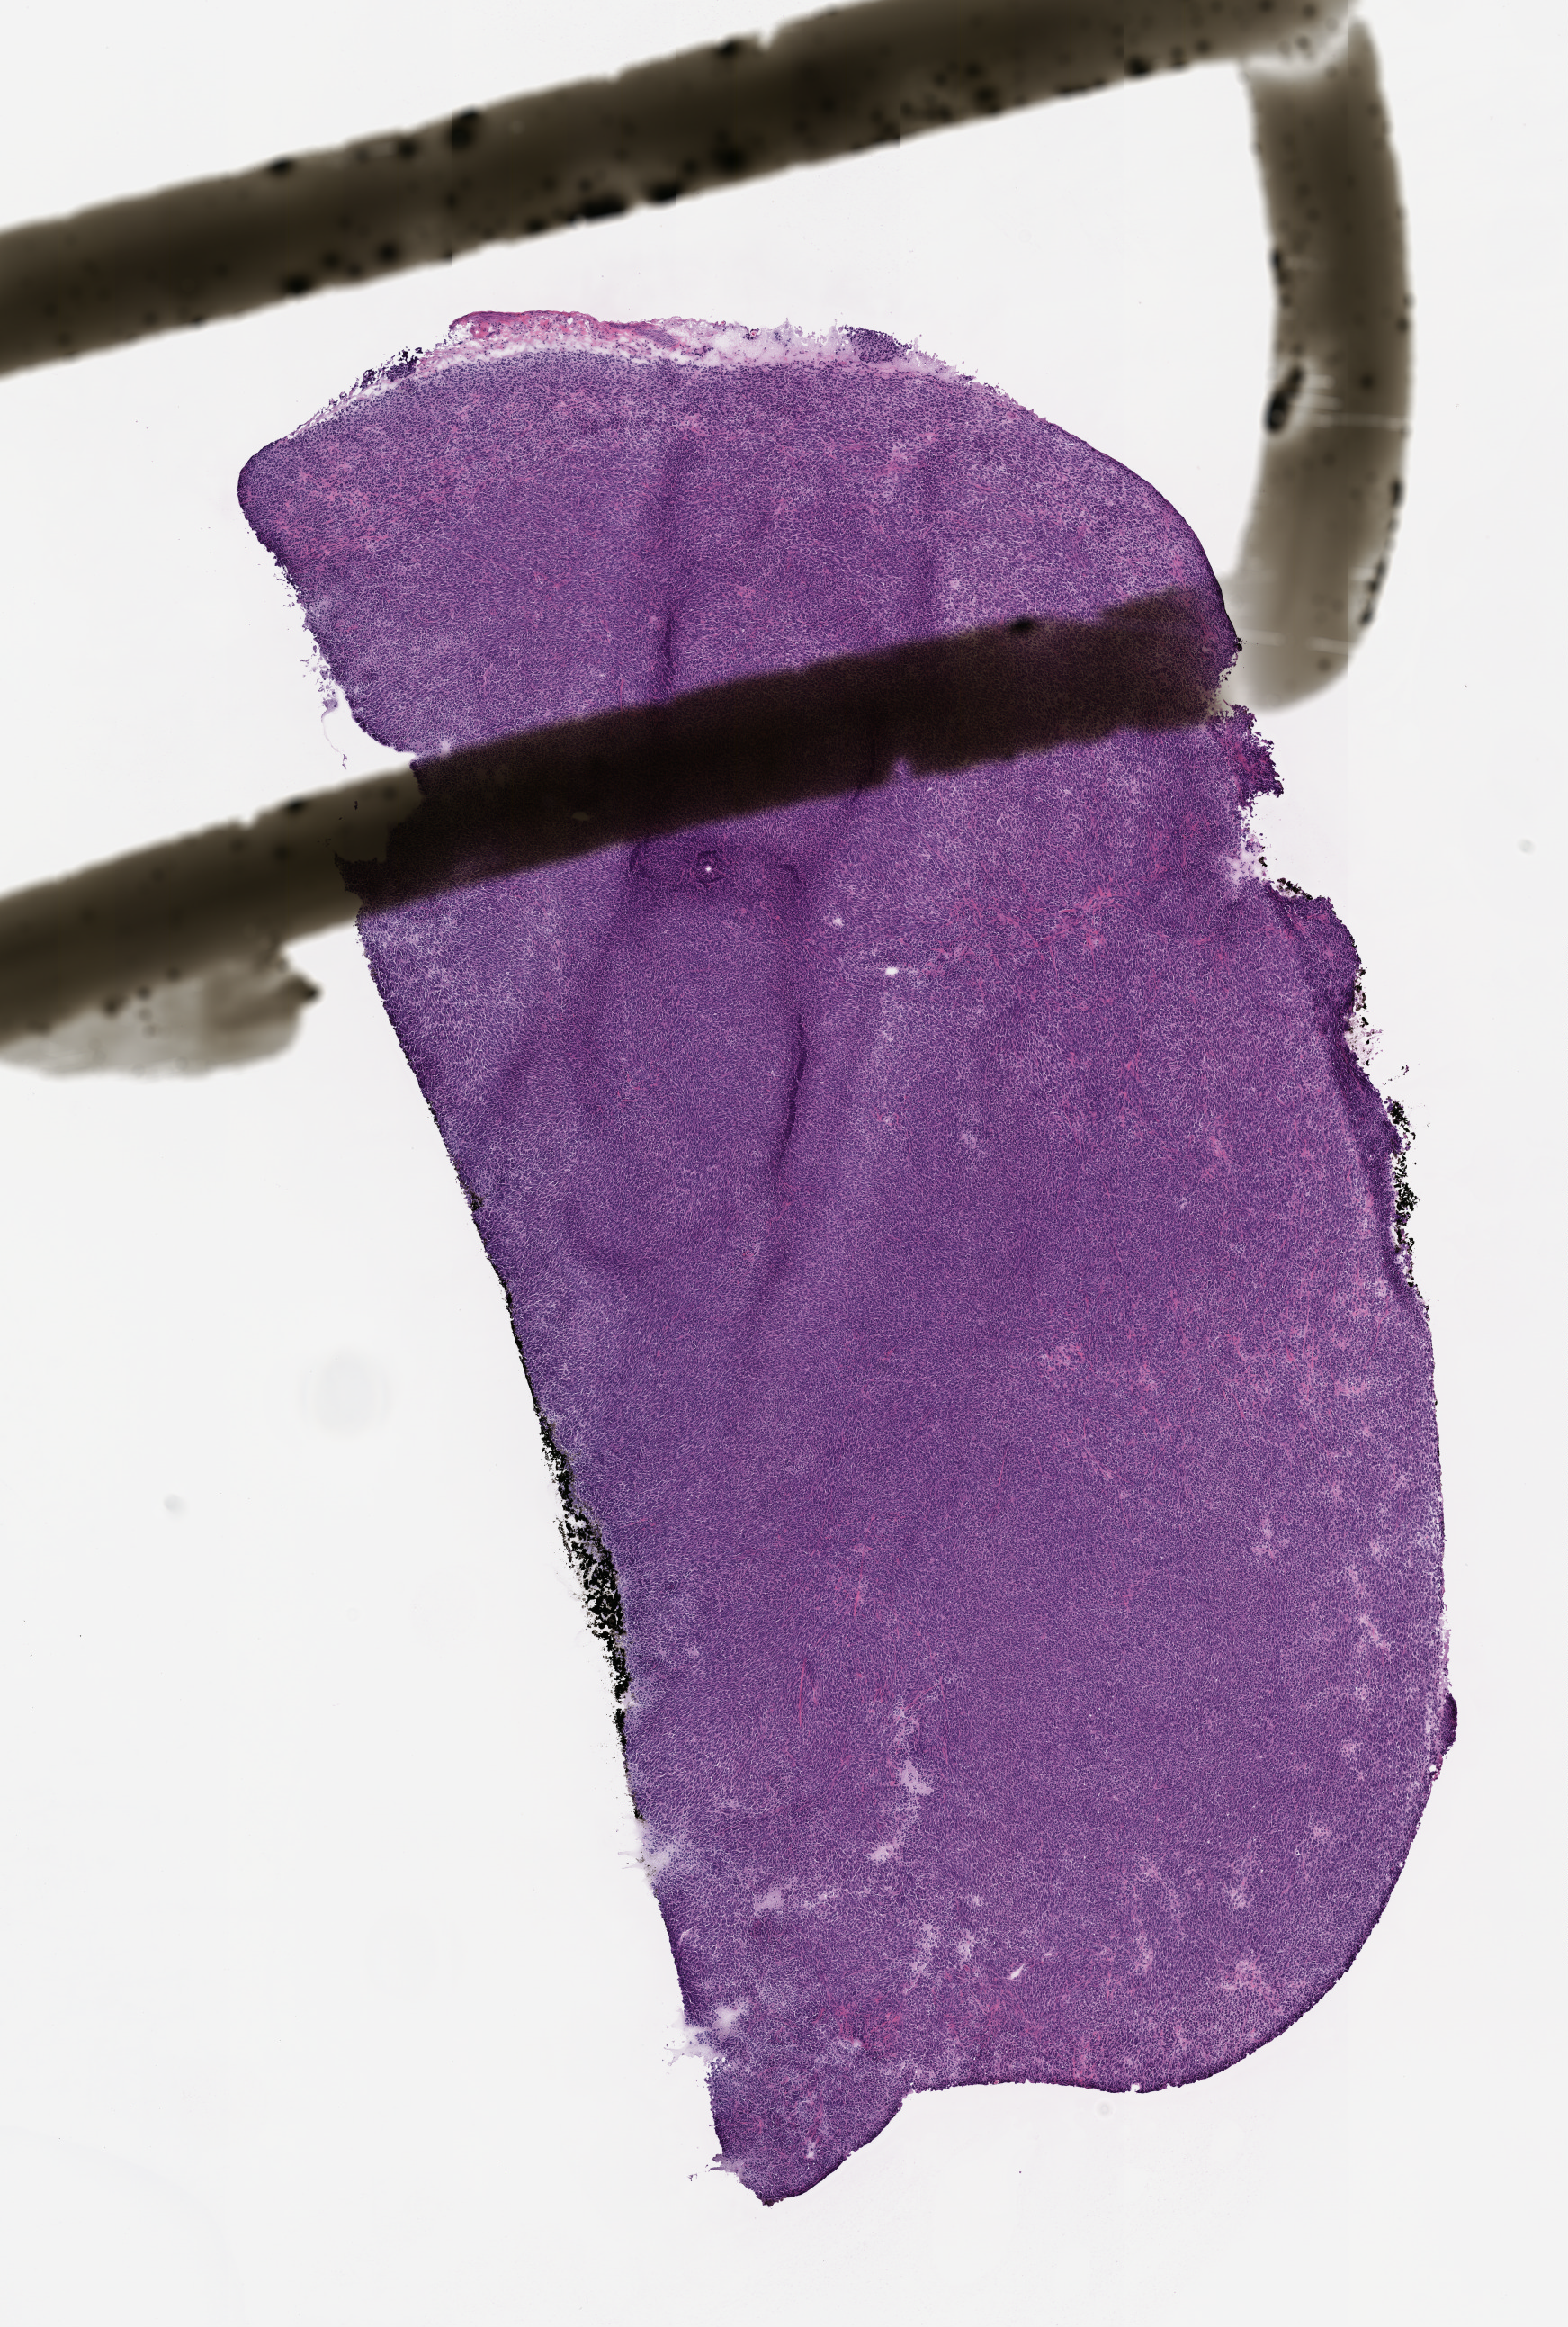
H&E whole-slide image of a patient-derived xenograft (PDX) tumor grown in a mouse, a low-resolution overview of the entire scanned area, about 7.0 x 10.4 mm. Formalin-fixed, paraffin-embedded (FFPE) tissue. Originating tumor site category: skin.
- originating patient diagnosis: Melanoma